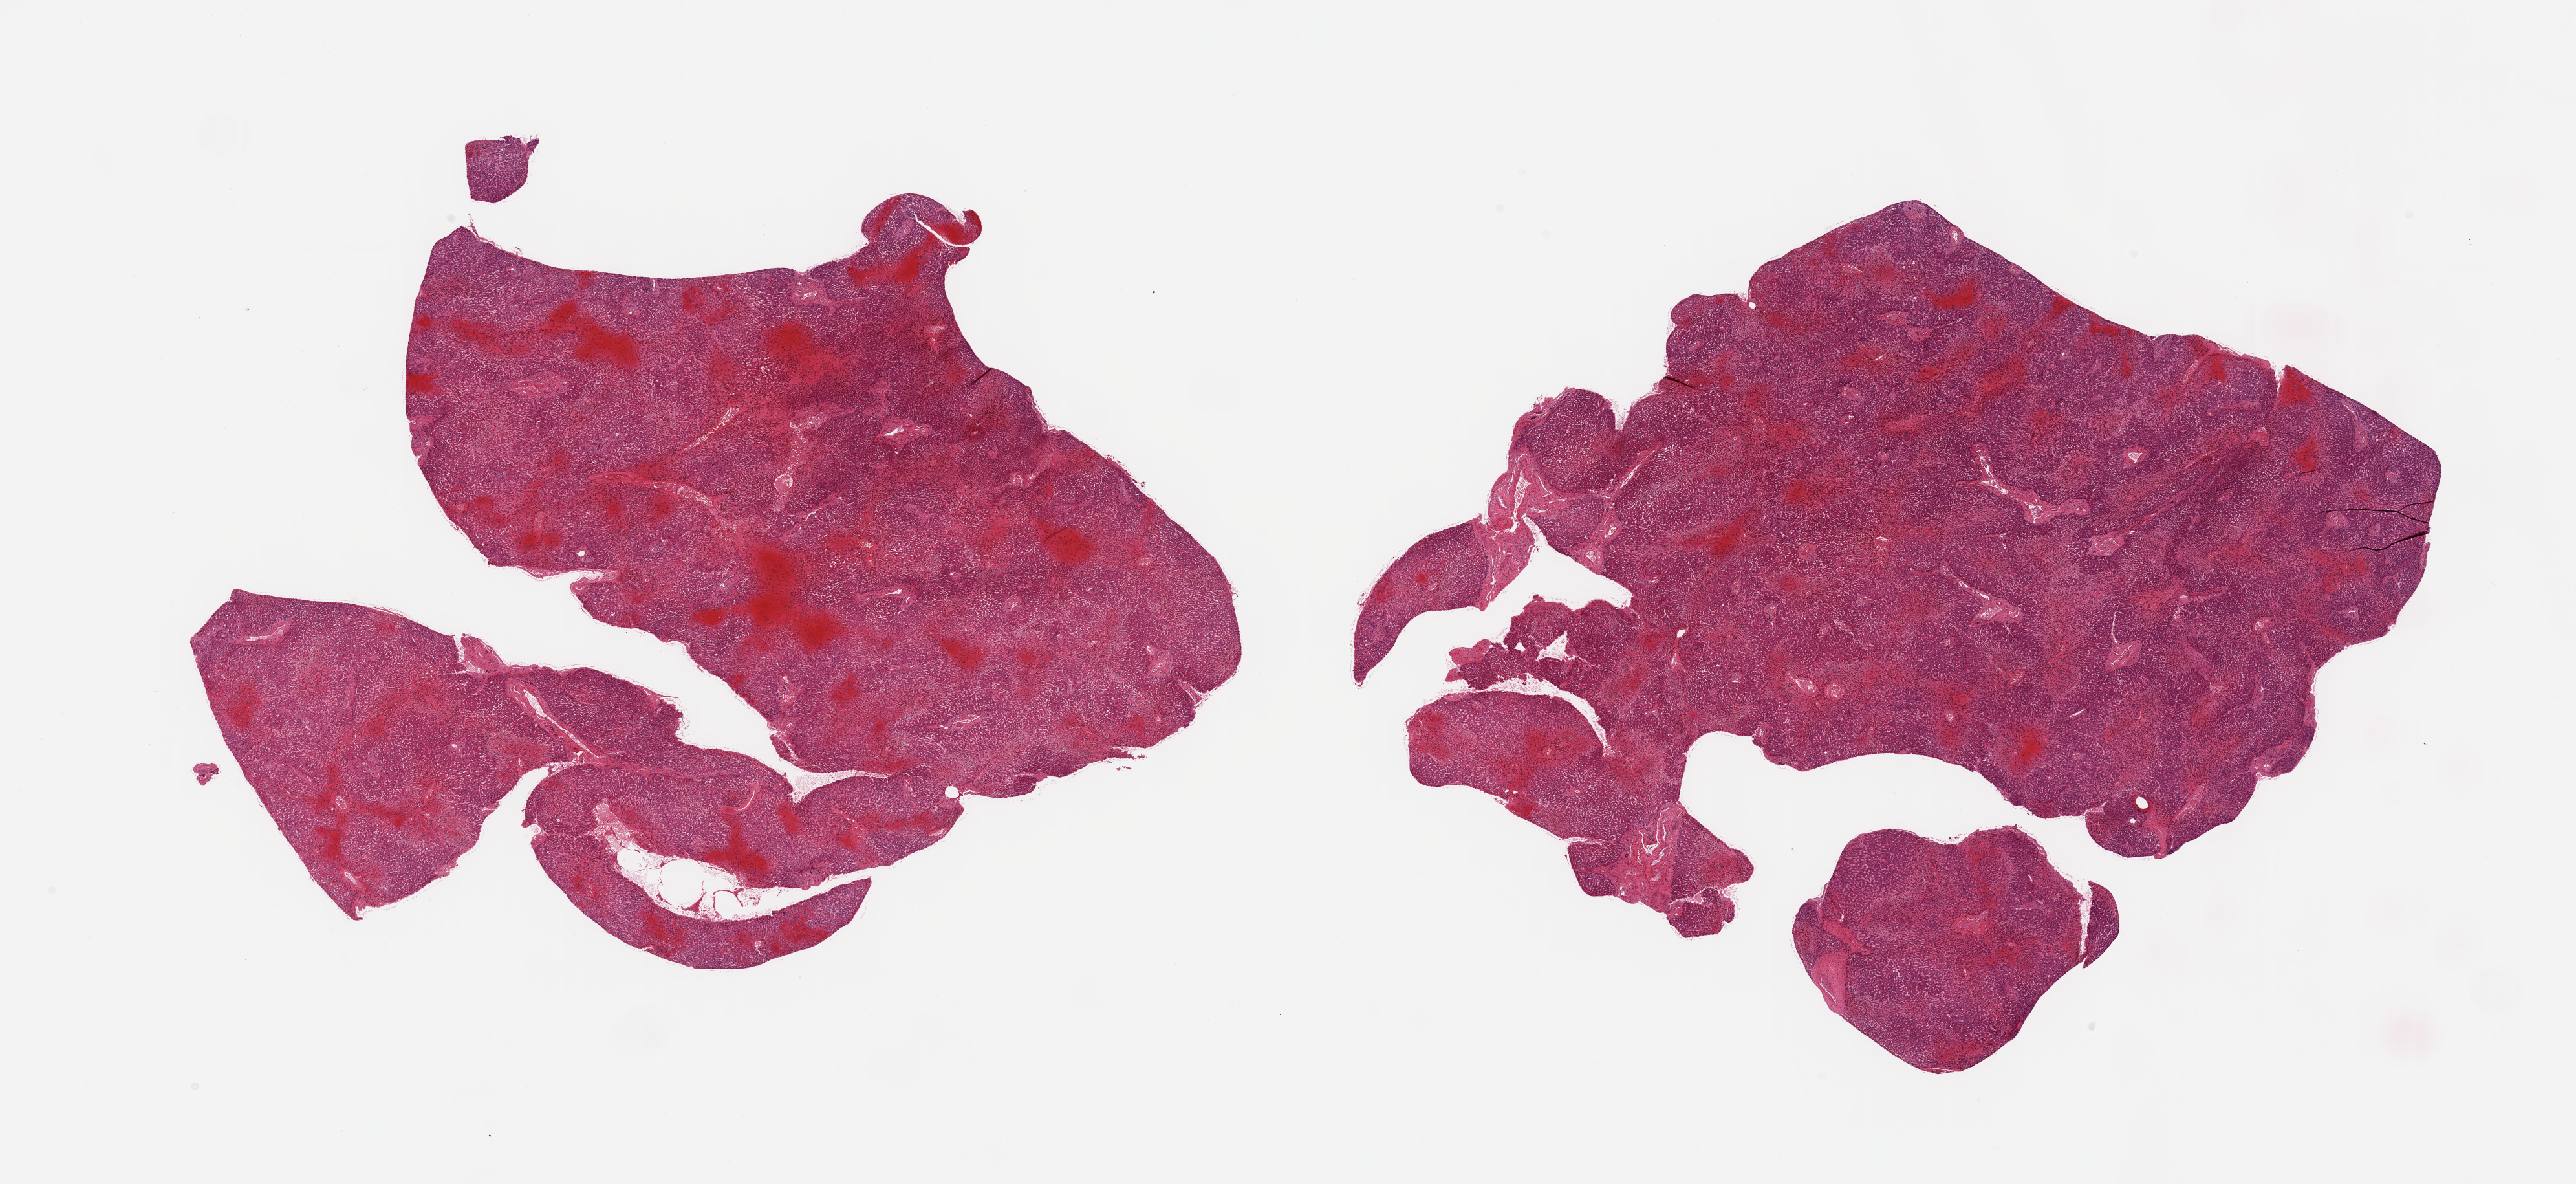
Haematoxylin and eosin whole-slide image — a low-resolution overview of the entire scanned area, about 31.5 x 14.5 mm; PAXgene-fixed paraffin-embedded (PFPE) section; section of liver (target tissue); donor tissue sample. Male donor.
- pathologist's review note for this sample: 2 pieces; severe central vascular congestion and atrophy